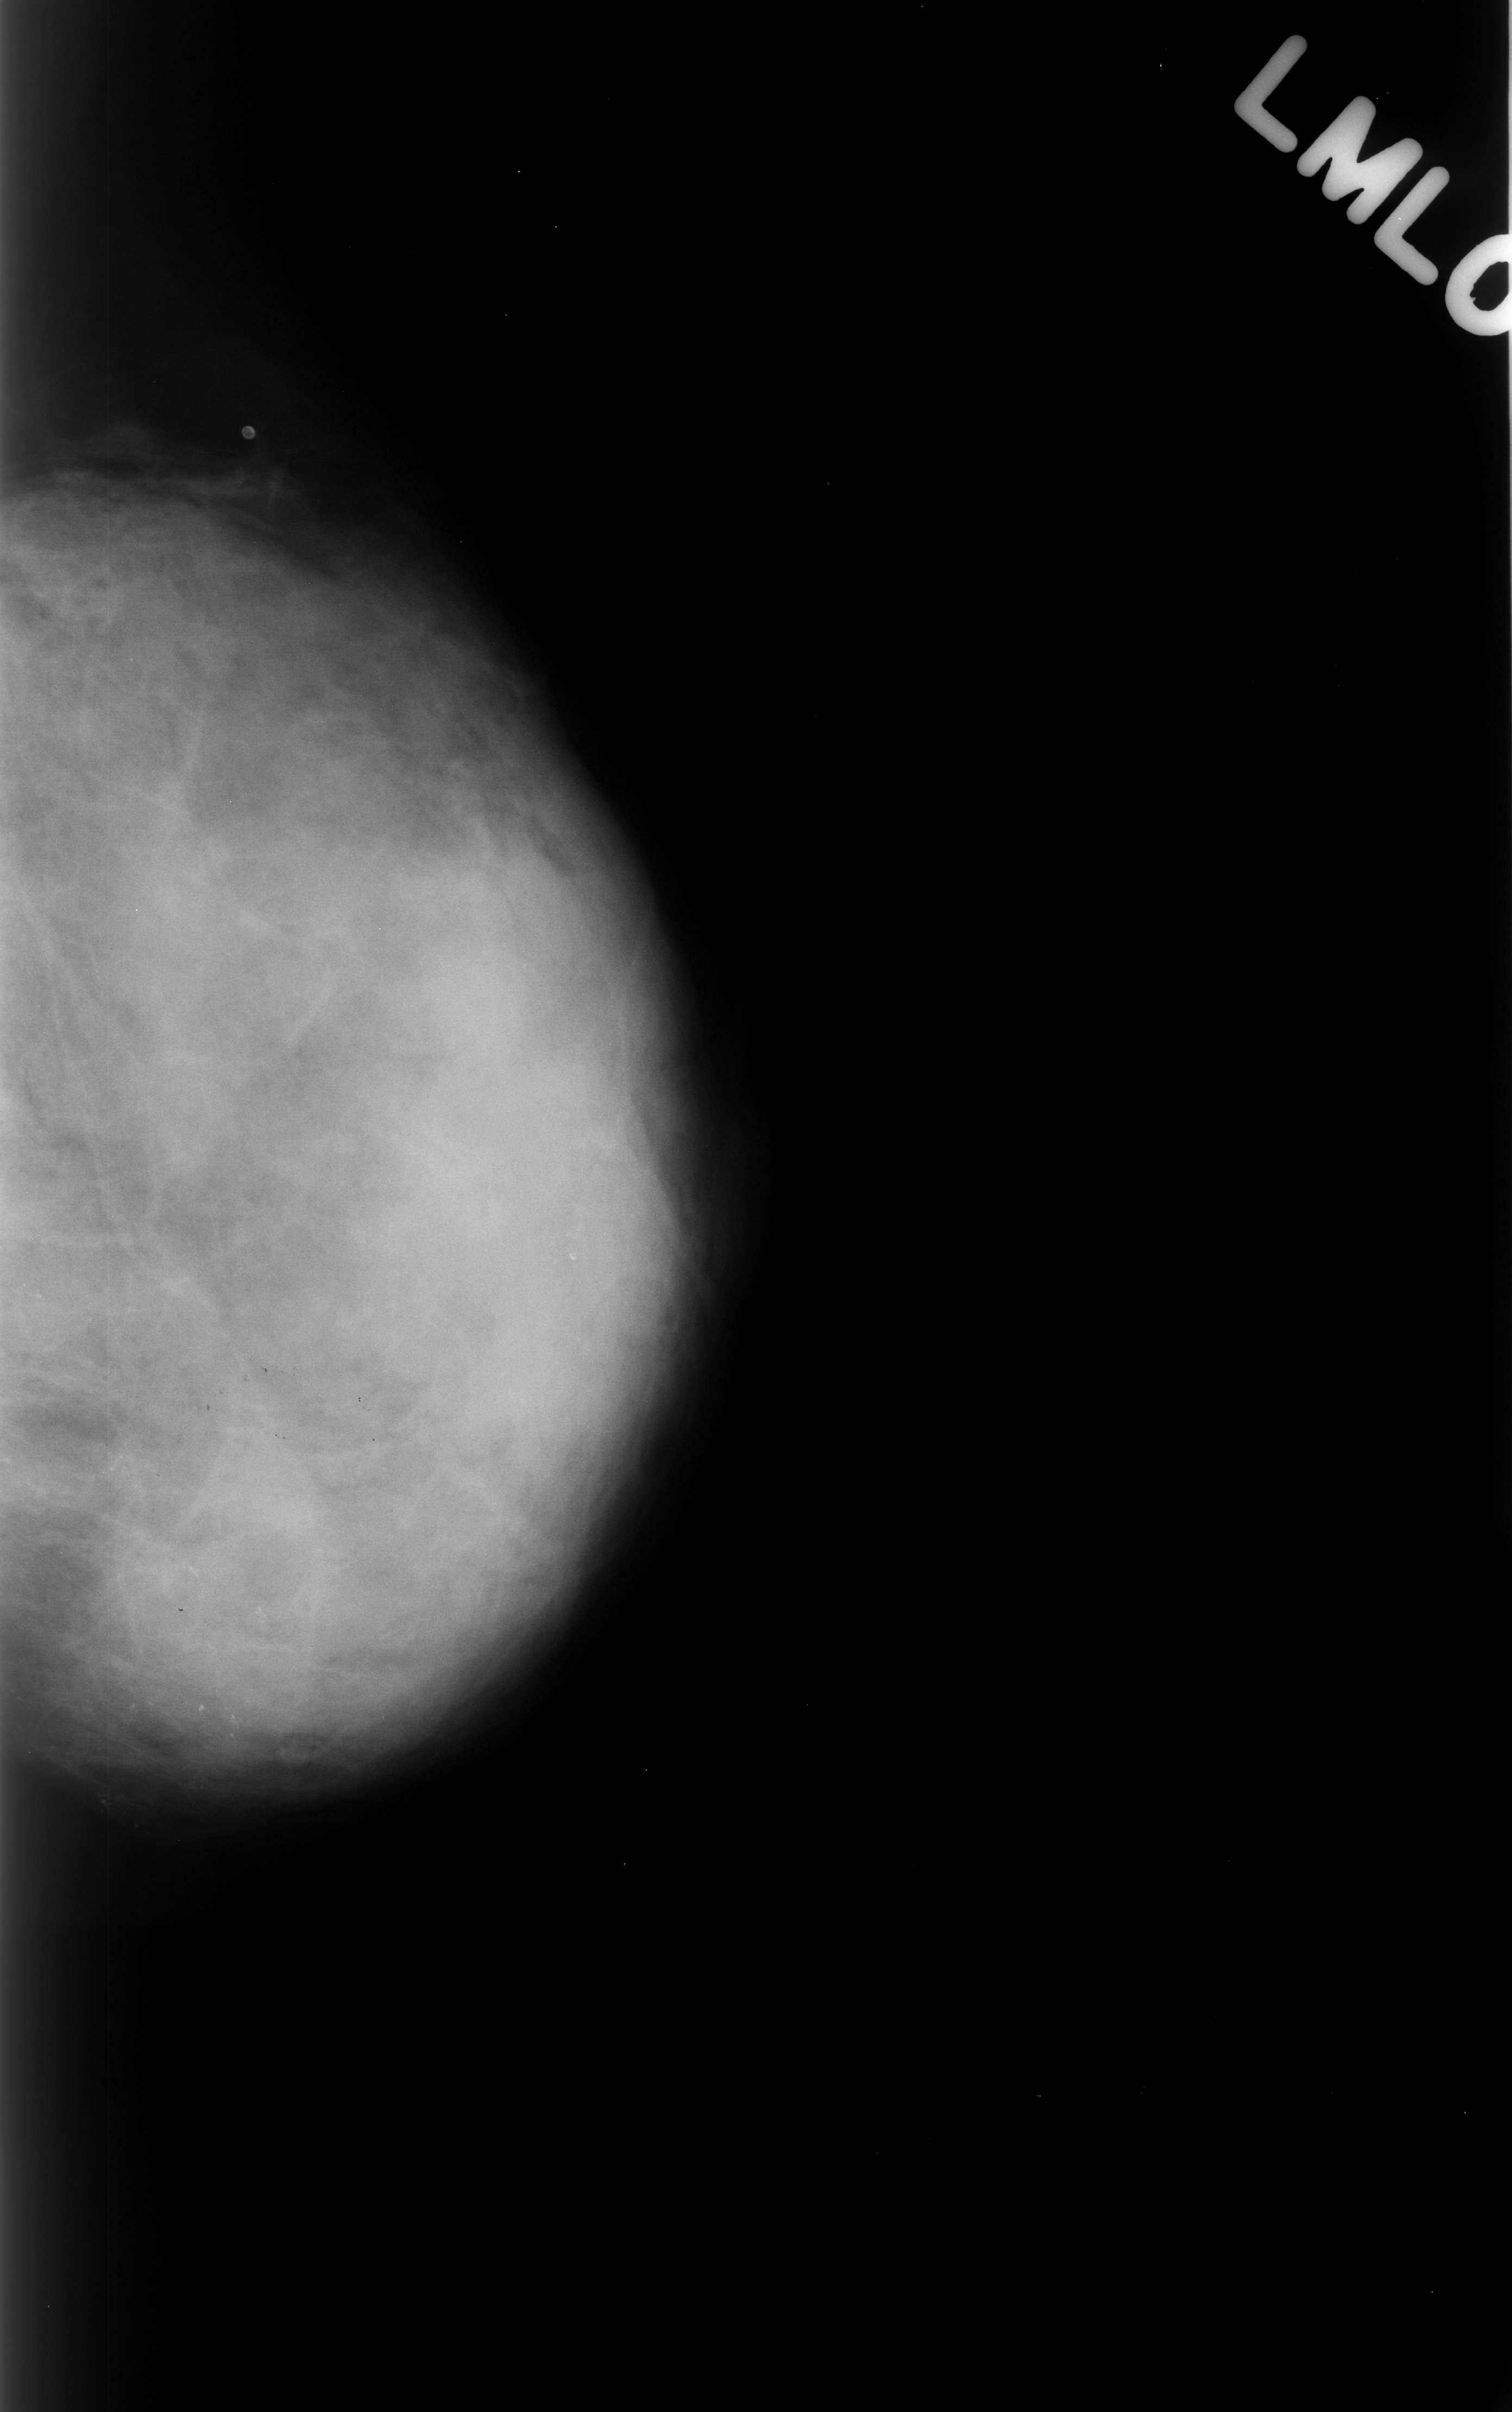
Mammogram (digitized film). Left breast. Mediolateral oblique (MLO) view. Breast composition: extremely dense (BI-RADS density category 4 of 4). 1512 × 2412 image matrix.
Expert-marked regions of interest on this film, with their recorded descriptors:
- calcifications, morphology pleomorphic, distribution segmental; BI-RADS assessment category 4; subtlety rating 3 on a 1 (subtle) to 5 (obvious) scale; pathology (as recorded): benign: bounding box (x1, y1, x2, y2) in pixels: (0, 1360, 436, 1931)